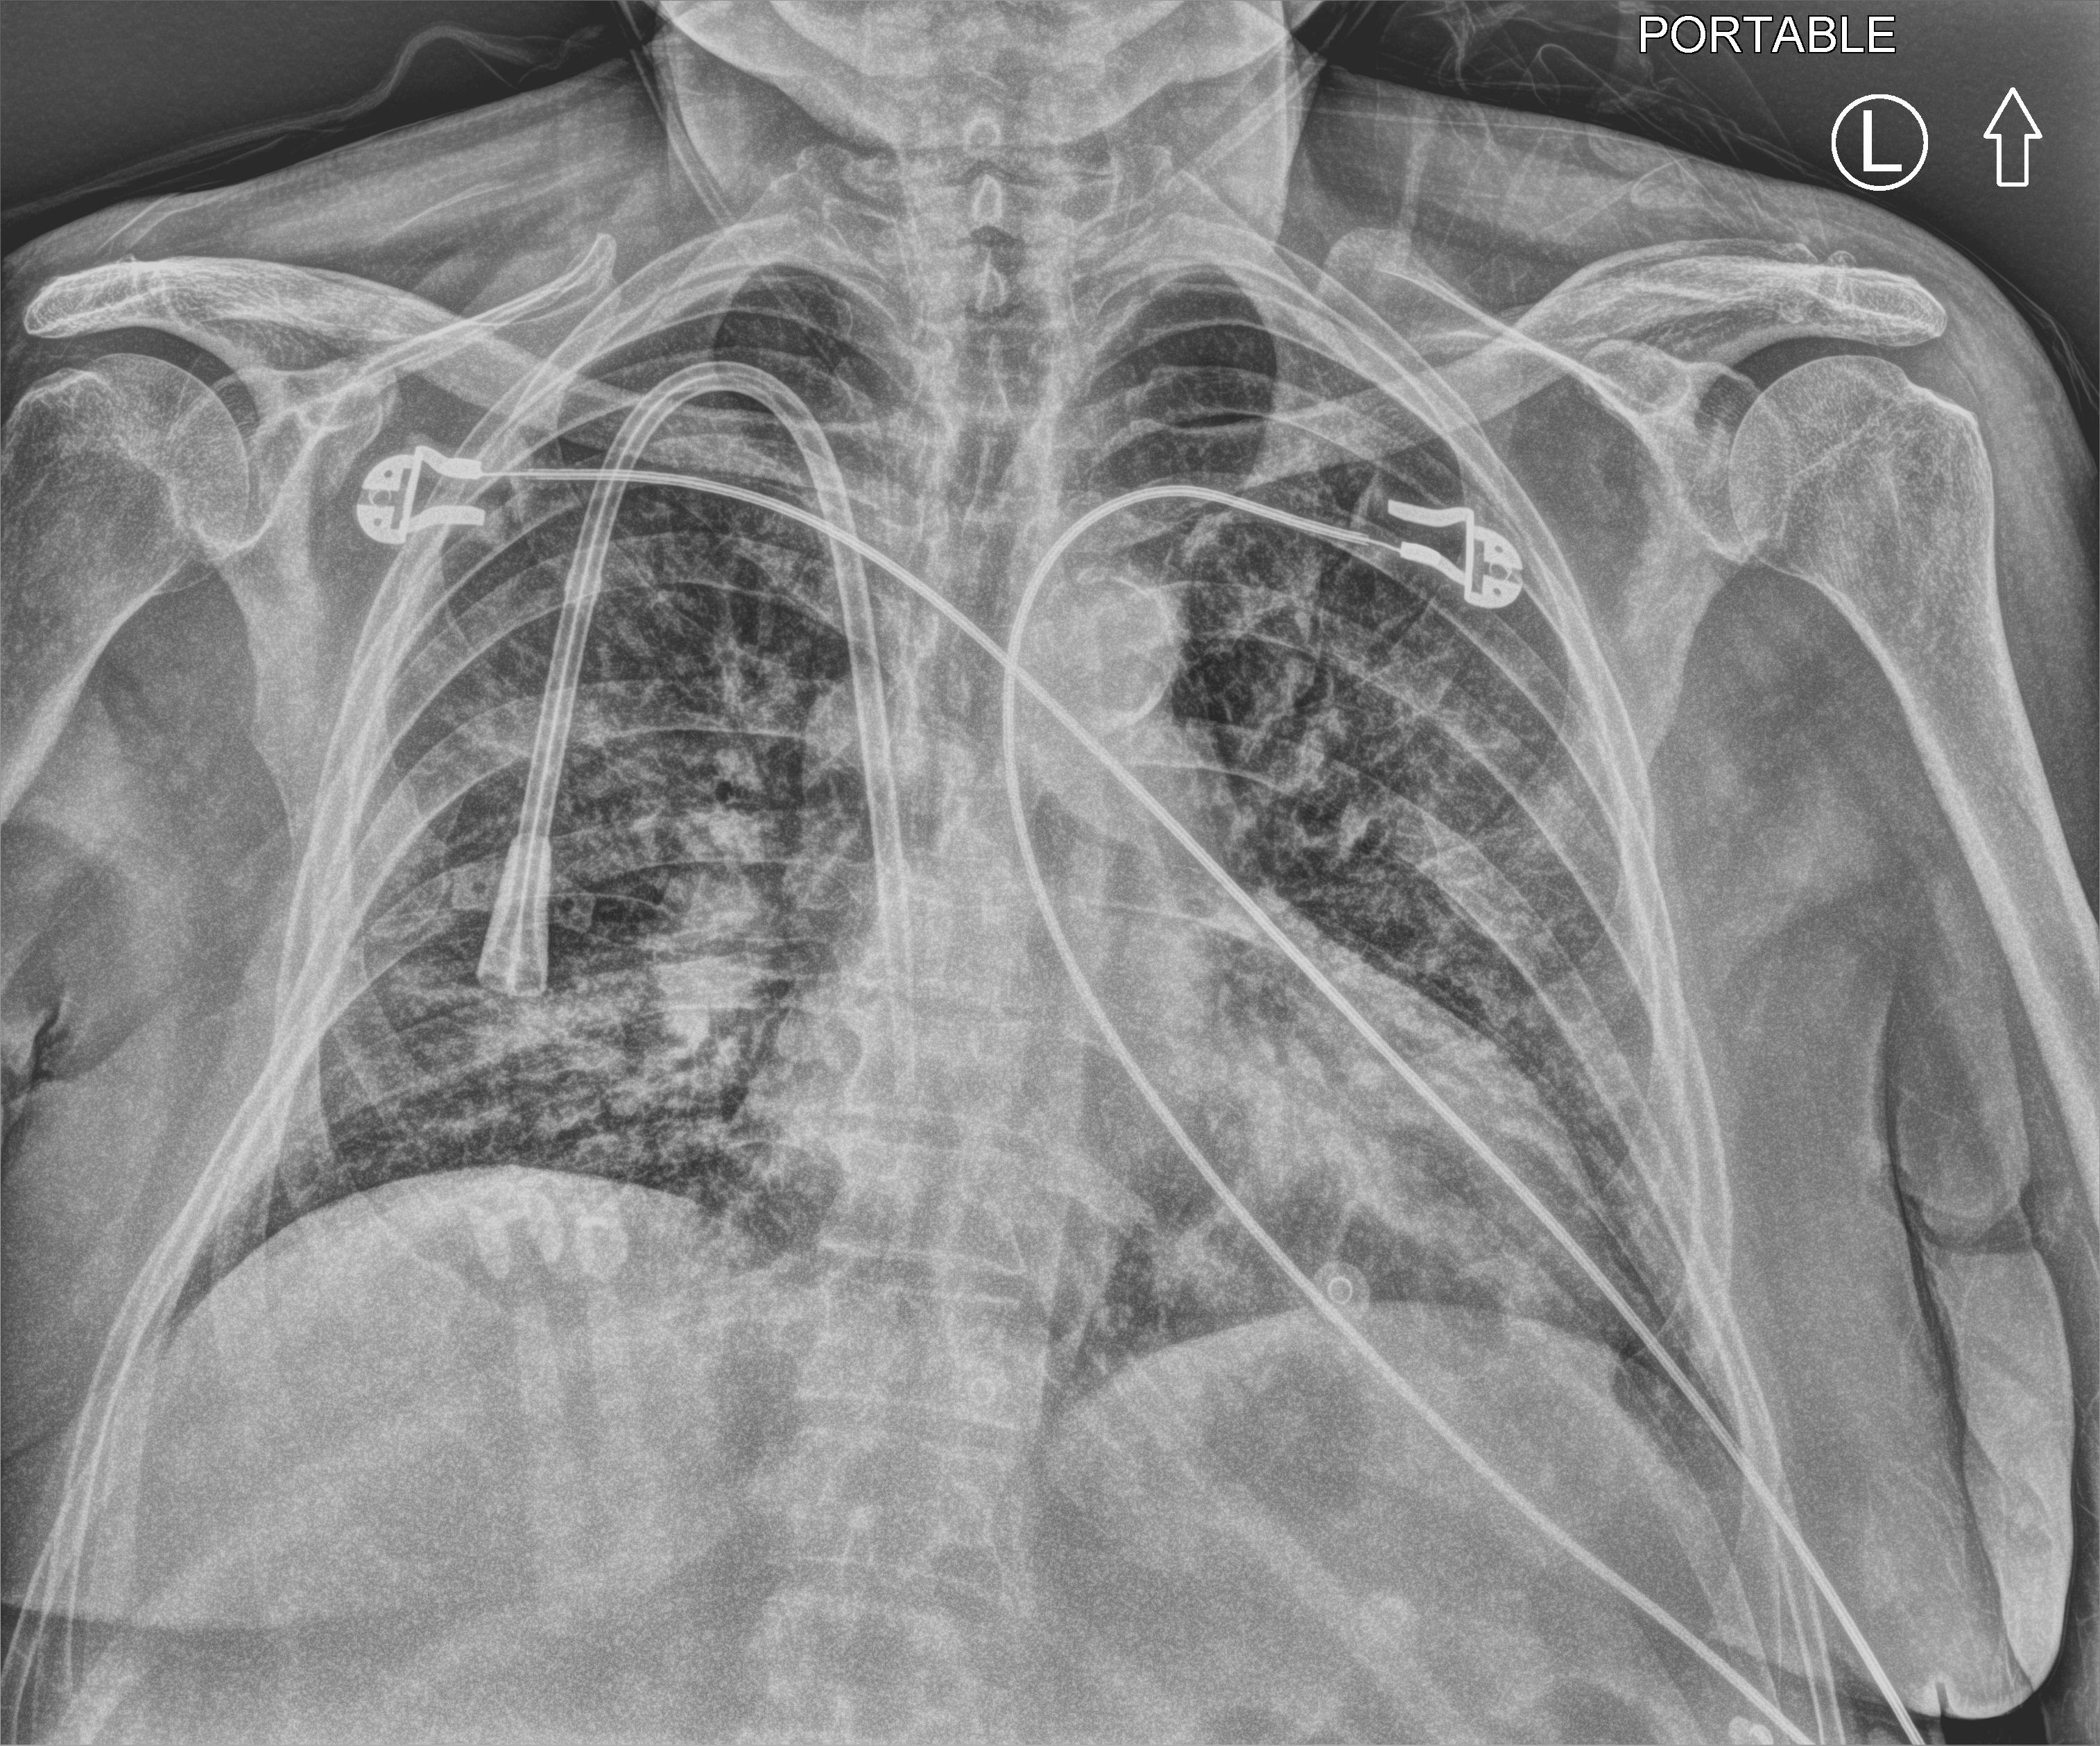
Chest X-ray (portable). Patient hospitalised with COVID-19; male, aged 60–74 years.
From the hospital-stay record, not from the radiograph (when in the stay this image was taken is not recorded): diabetes (admission record): yes; mechanically ventilated during this hospital stay: no; admitted to intensive care during this hospital stay: no.